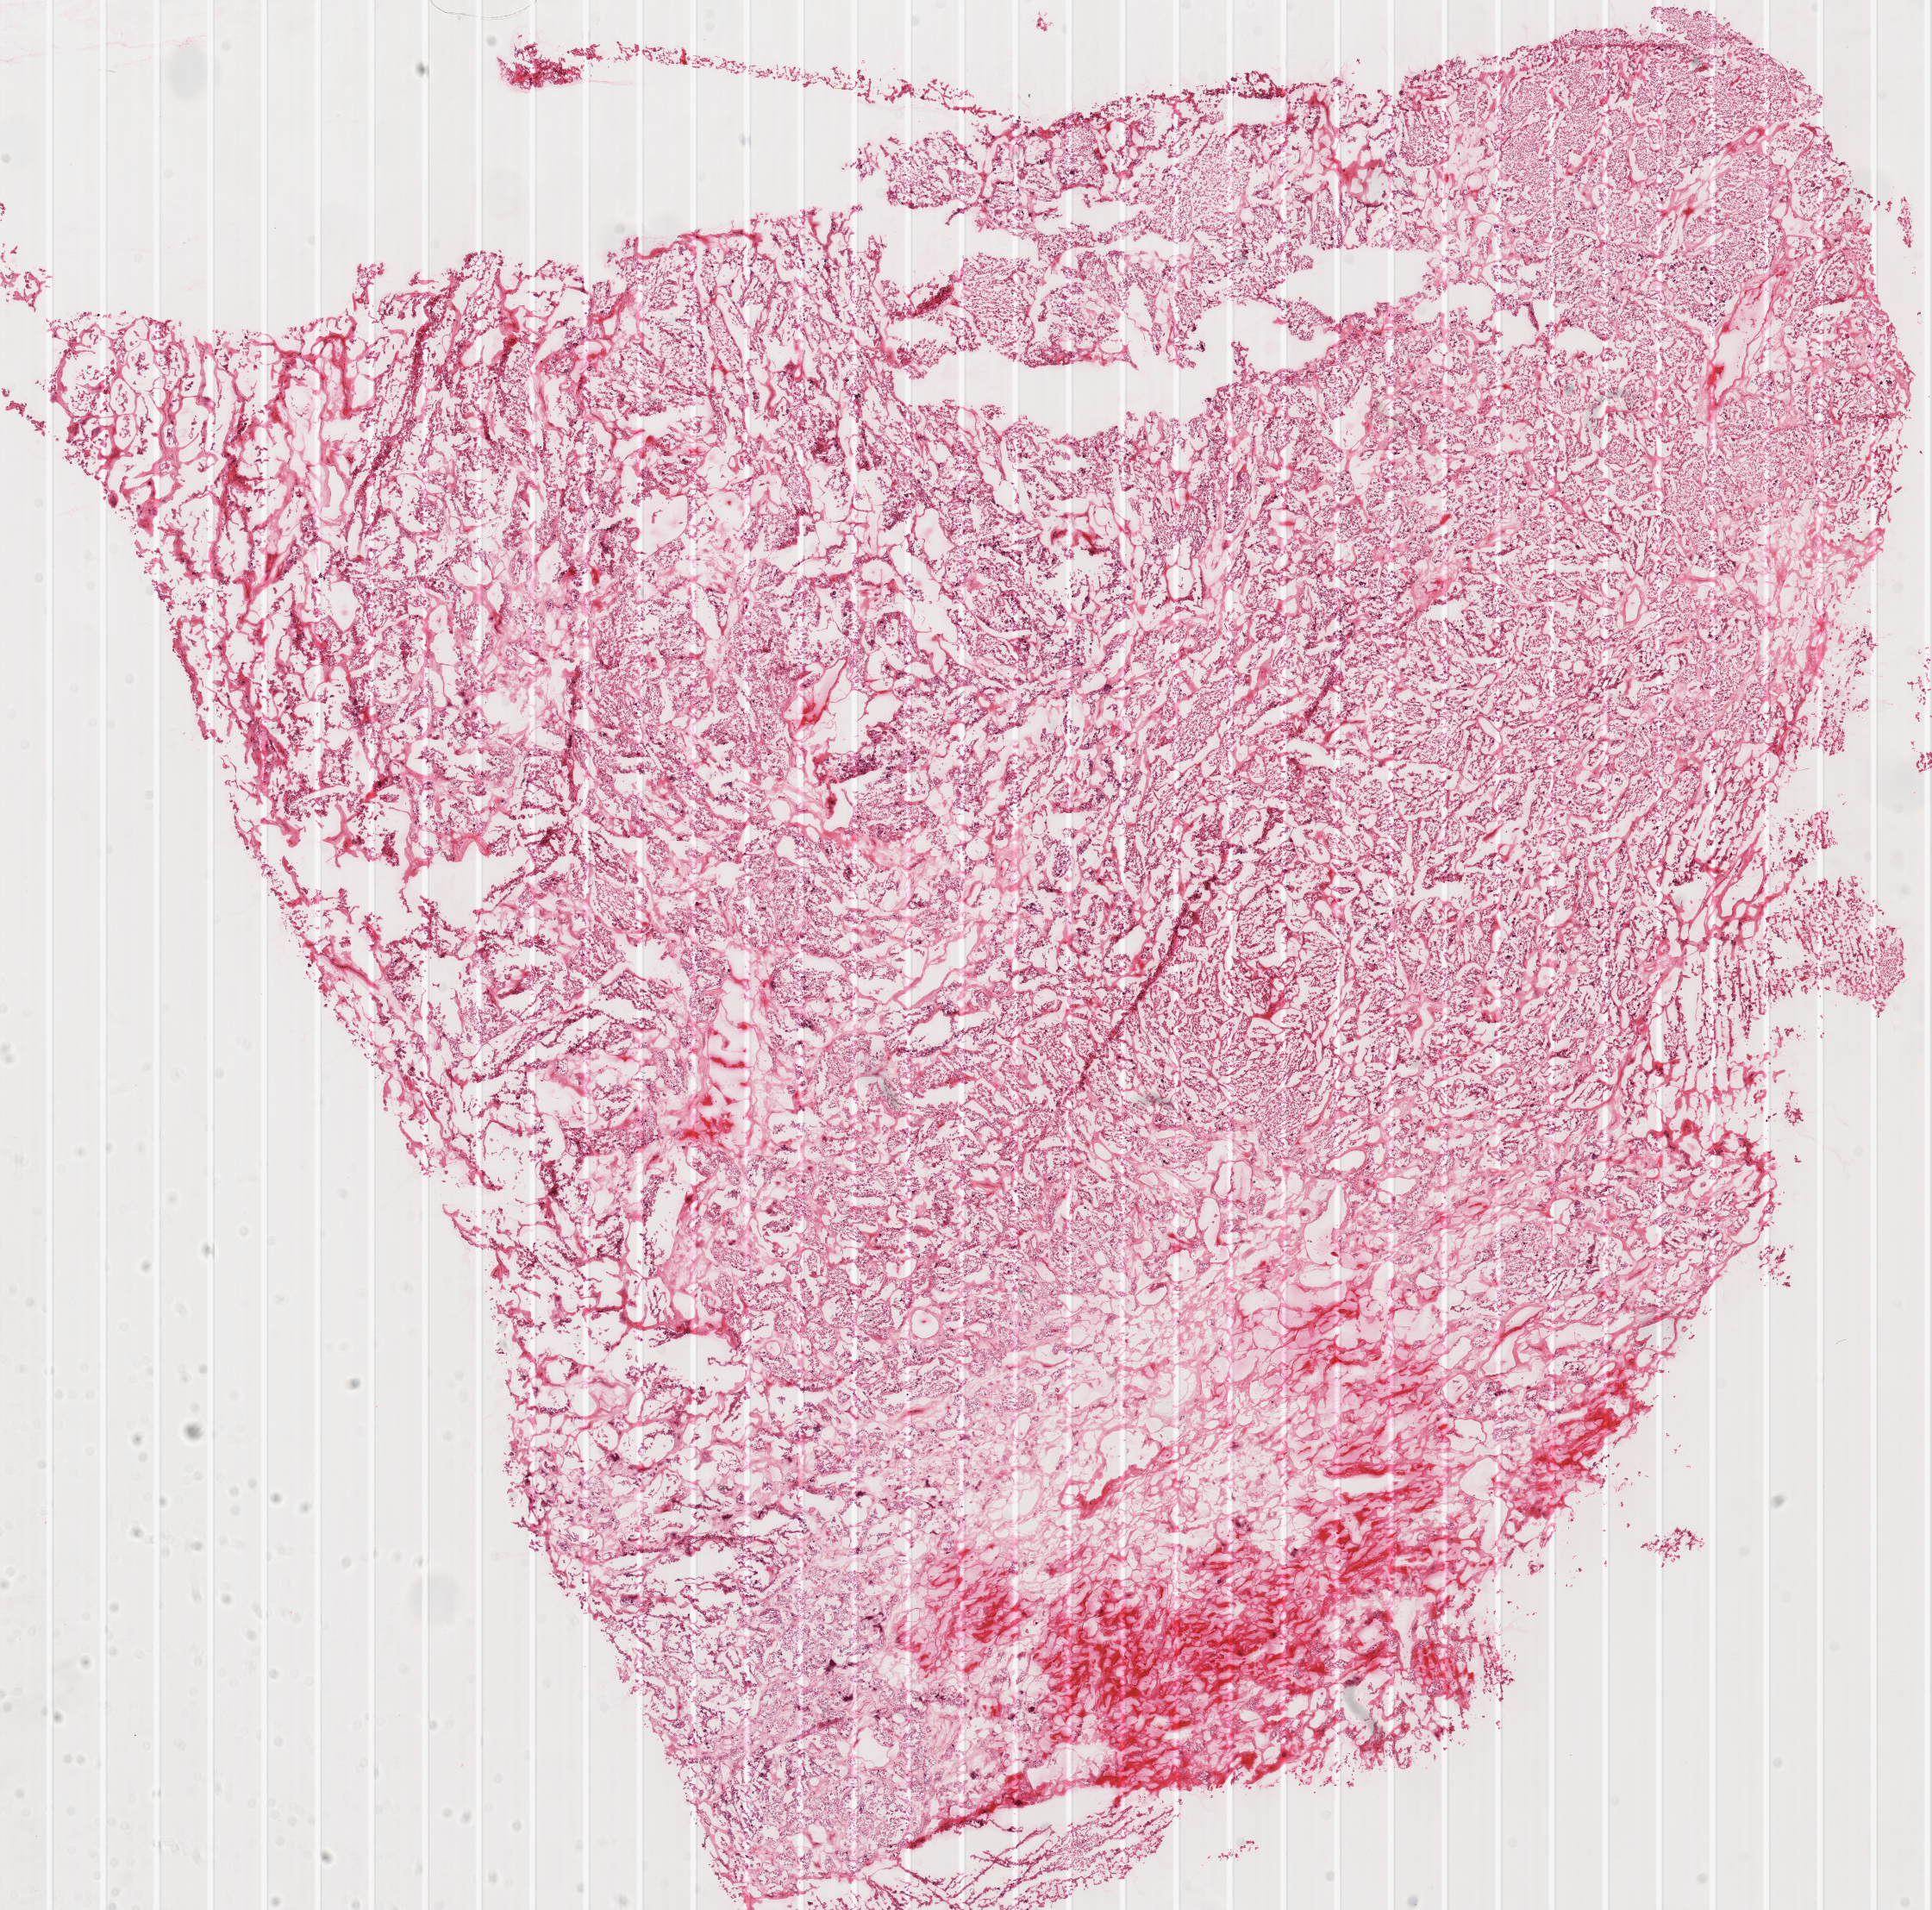
Whole-slide histology image, H&E, low-resolution overview of the scanned area, about 17.6 x 17.4 mm; frozen section; sample: primary tumour, kidney. Patient: female, age at initial diagnosis 38 years. Slide review estimates, as recorded: tumour cells 100%, tumour nuclei 90%.
Pathologic diagnosis: Renal cell carcinoma, chromophobe type.